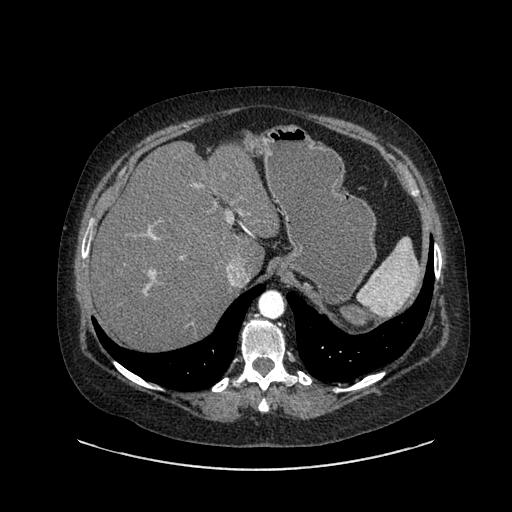
Contrast-enhanced abdominal CT, one axial slice. Slice 644 of 769 in the series (ordered by position). Reconstruction kernel SOFT. 120 kVp. Intravenous contrast given. Soft-tissue window (W 400 / L 40 HU). 0.62 mm slice thickness. 512 × 512 image matrix, field of view 460 × 460 mm. Patient: female, 61 years. From the clinical record (not read from this slice): diagnosis: adrenocortical carcinoma; tumour side: left adrenal; tumour size at pathology: 13 cm; Ki-67 index: 79 %; stage (as recorded): 2.
Outlined on this slice (semi-automatic segmentation, software-assisted and operator-edited):
- mass: bounding box (x1, y1, x2, y2) in pixels: (337, 303, 369, 331)